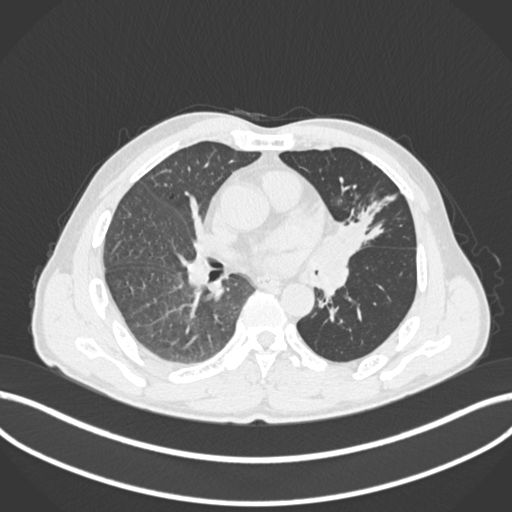
Chest CT, one axial slice; slice 95 of 255 in the series (ordered by position); 120 kVp; lung window (W 1500 / L -600 HU); 1 mm slice thickness; 512 × 512 image matrix, field of view 400 × 400 mm. Patient: male, 57 years. Case-level facts recorded for this patient, not image findings: clinical TNM (as recorded): T2b N0 M0.
Outlined on this slice (bounding box drawn by a radiologist):
- lung tumour (recorded histology: squamous cell carcinoma): bounding box [x1, y1, x2, y2] px = [324, 208, 365, 277]